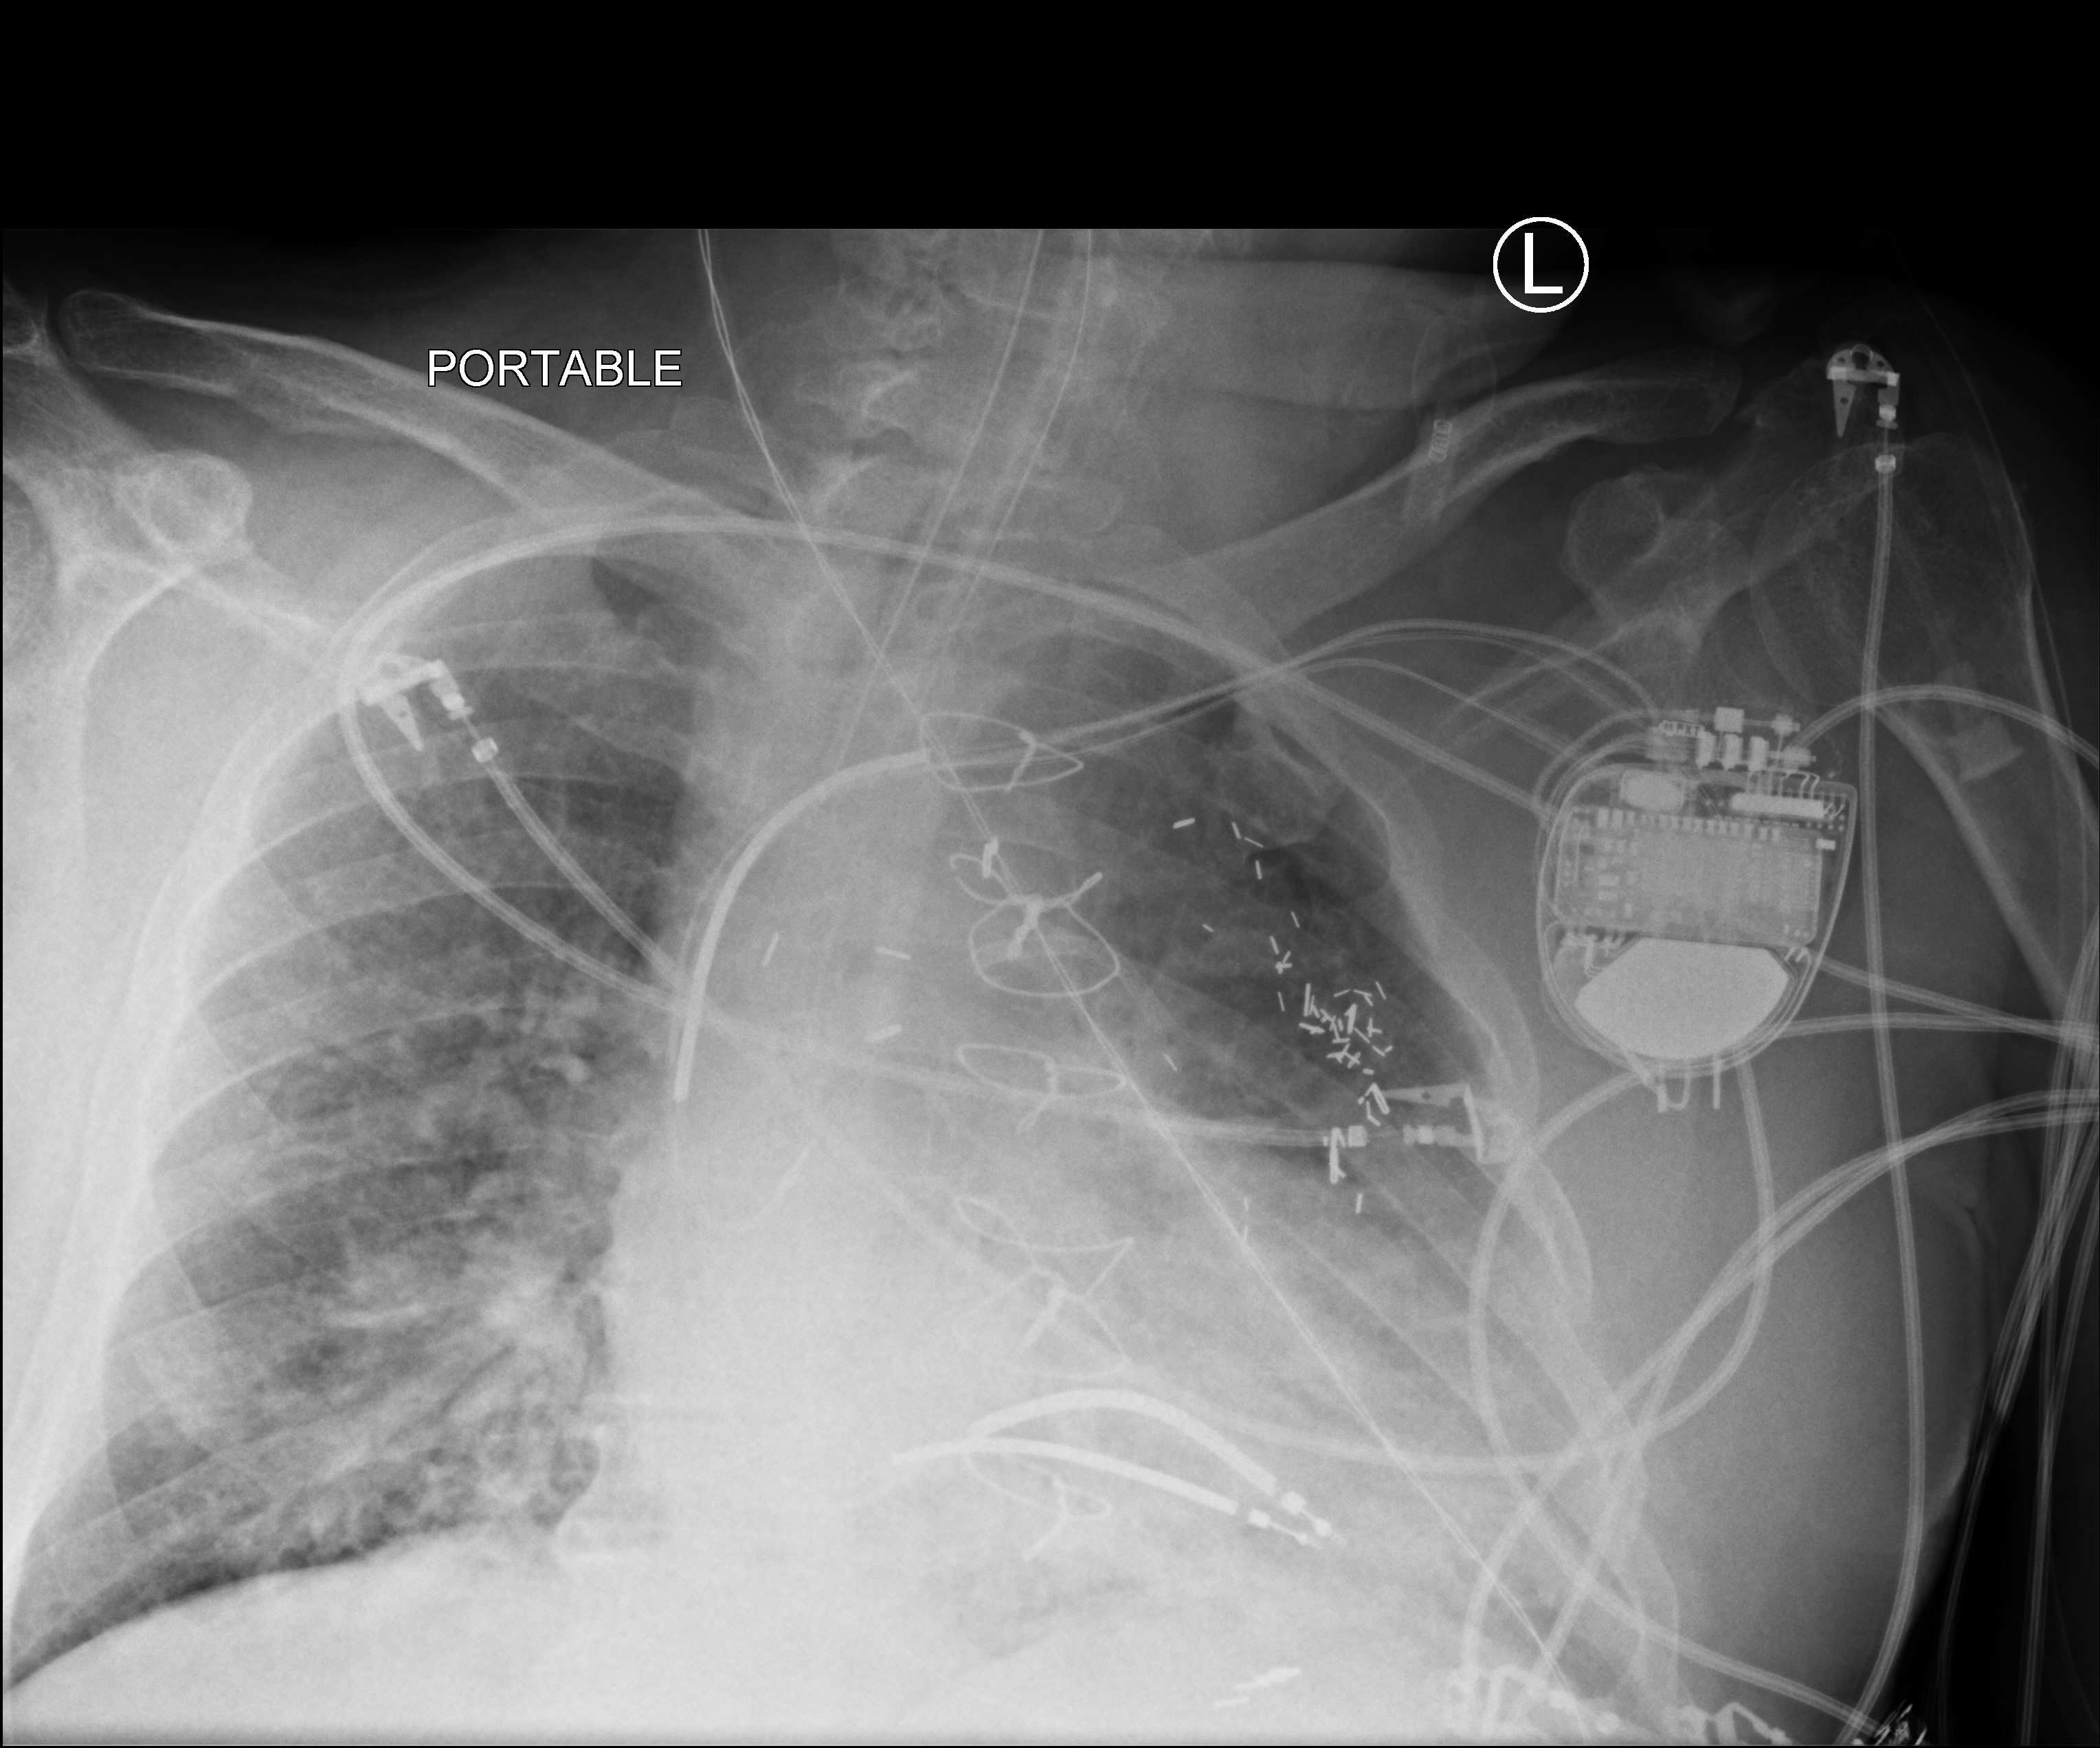
Chest X-ray (portable), anteroposterior (AP) projection. Patient hospitalised with COVID-19; male, aged 60–74 years.
Hospital-stay facts (about this admission, not read from this image; timing relative to this image not recorded): mechanically ventilated during this hospital stay: yes; diabetes (admission record): yes; admitted to intensive care during this hospital stay: yes.